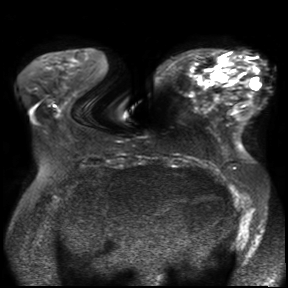
Breast MRI, one axial slice. Position 10 of 30 along the scan axis. Diffusion-weighted series; image 2 of 4 stored at this slice position (different b-values; order by instance number). 3 T. 4 mm slice thickness. 288 × 288 image matrix, field of view 360 × 360 mm. Female patient.
Outlined on this slice (manually delineated by an expert):
- tumour on diffusion-weighted imaging: bounding box (x1, y1, x2, y2) in pixels: (213, 58, 229, 79)